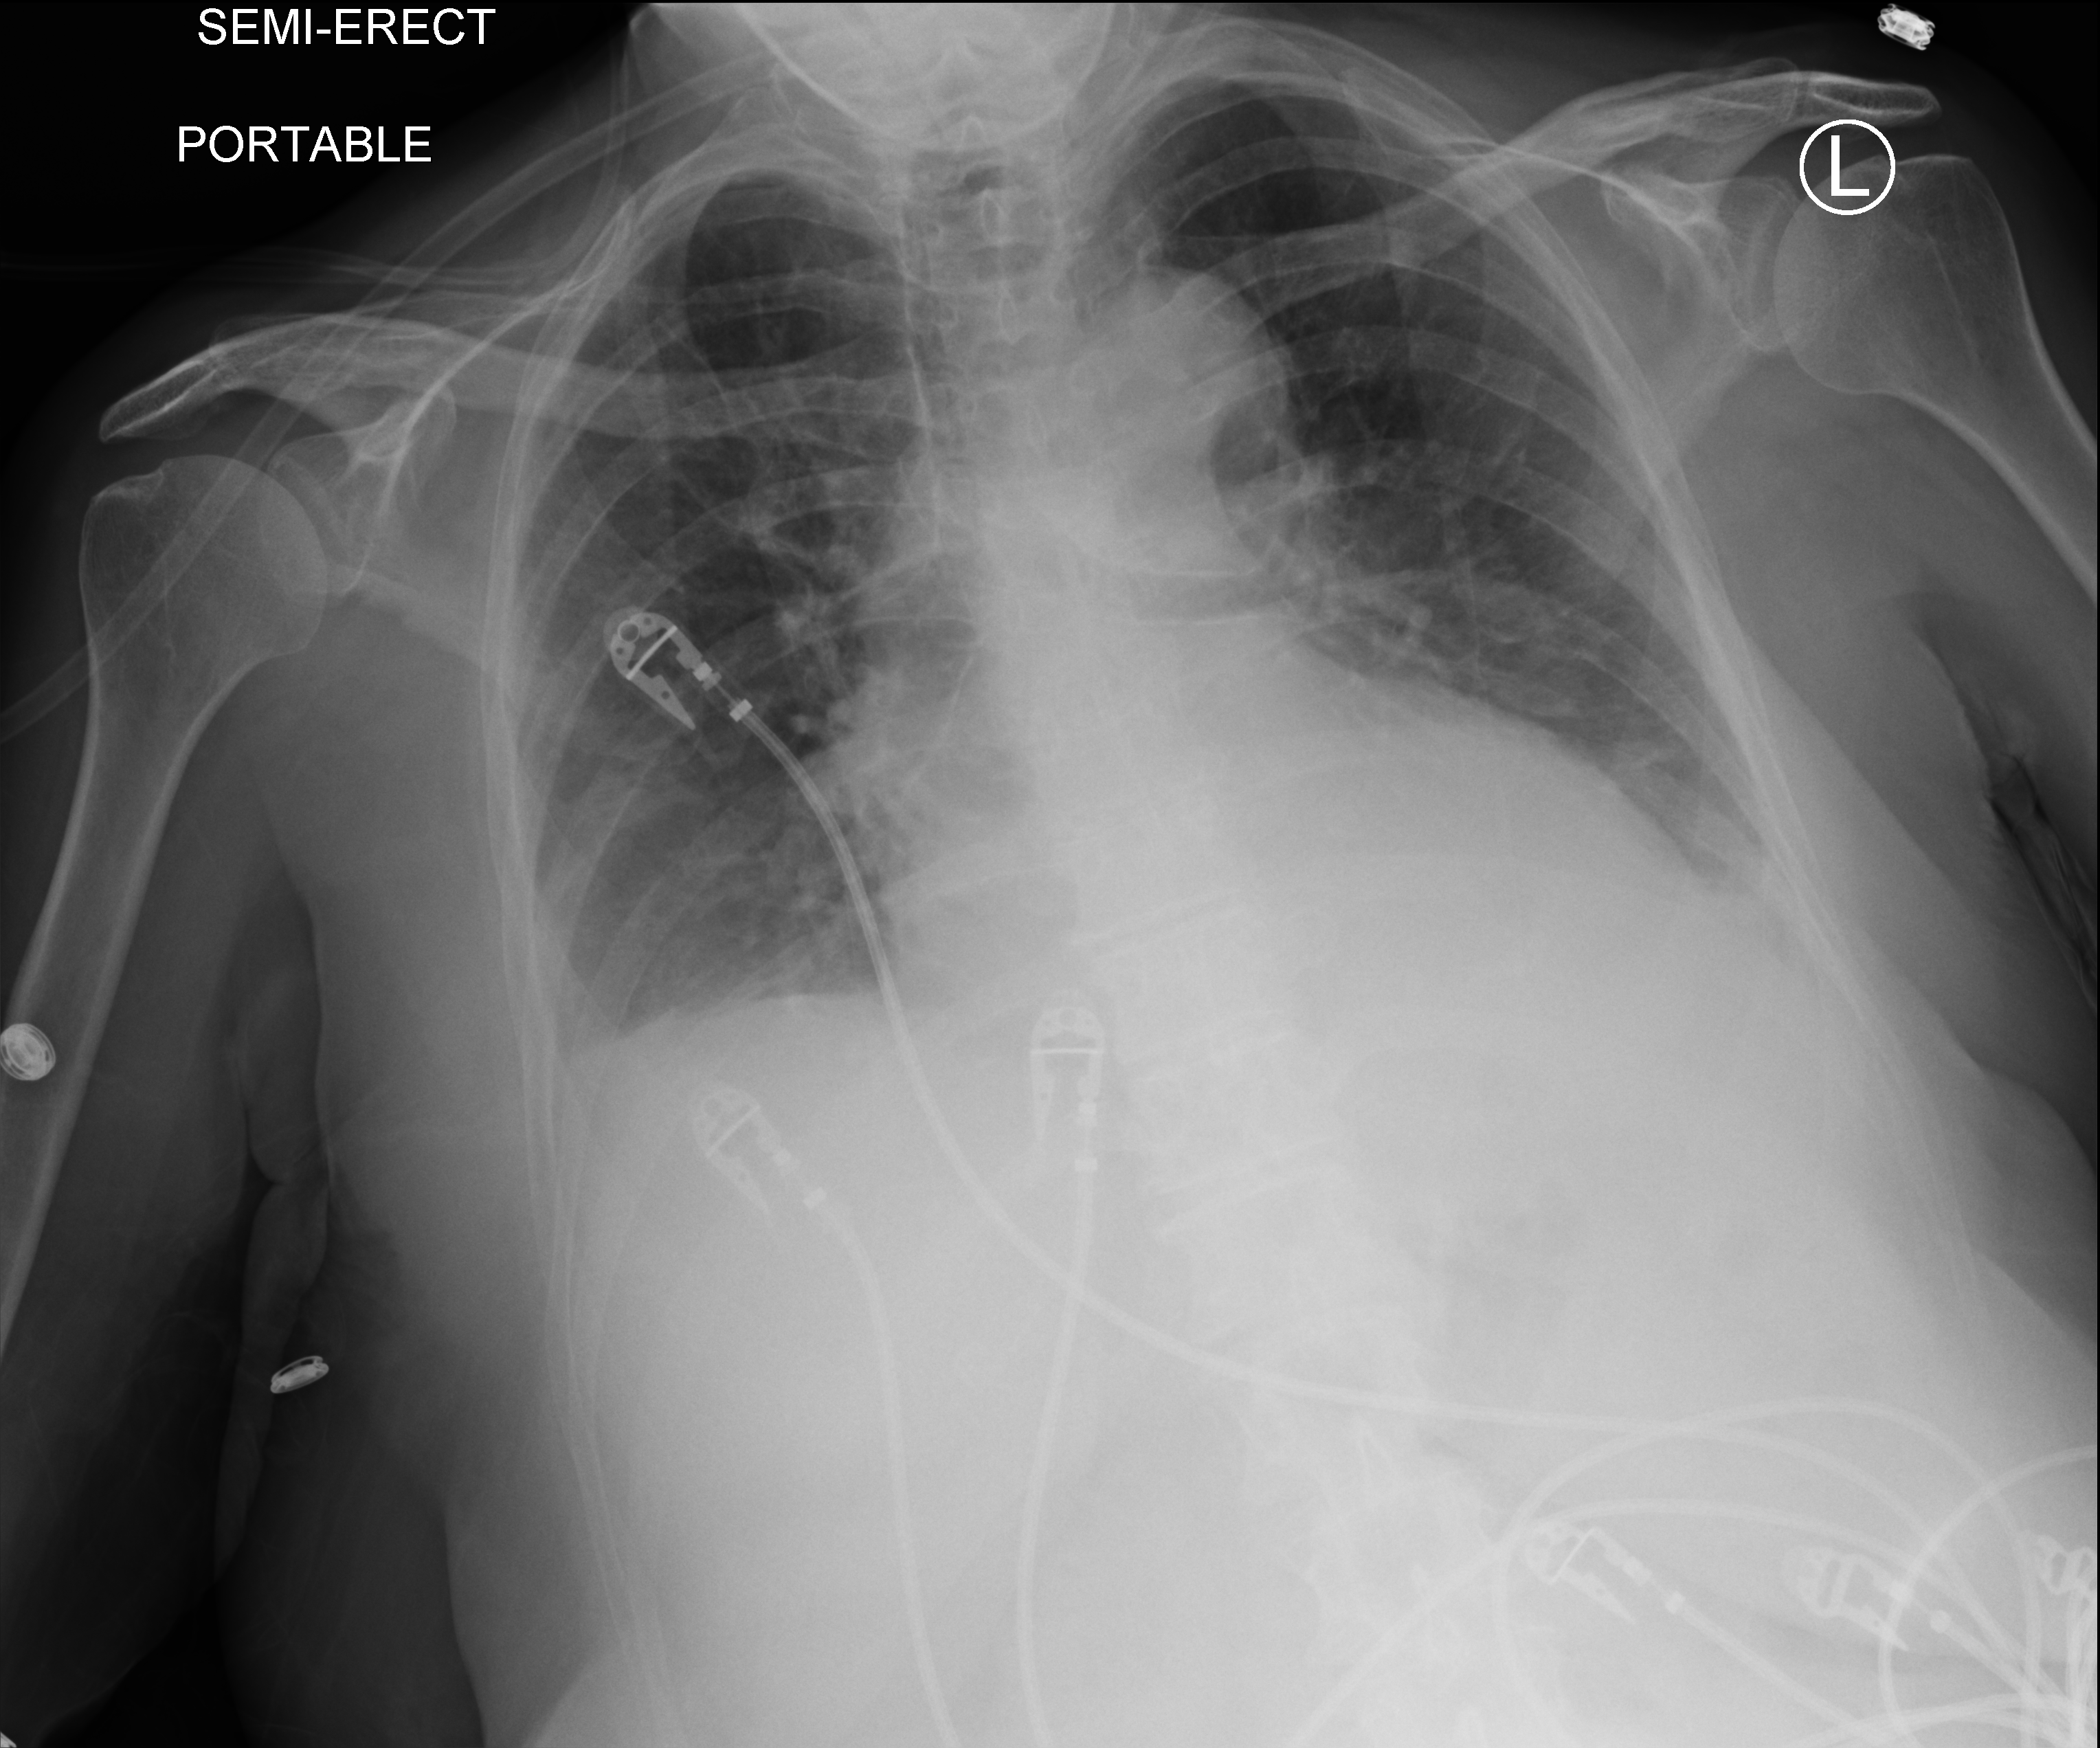
Portable chest radiograph, anteroposterior (AP) projection. Patient hospitalised with COVID-19; female, aged 75–90 years.
Hospital-stay facts (about this admission, not read from this image; timing relative to this image not recorded): mechanically ventilated during this hospital stay: no; length of hospital stay: 21 days; admitted to intensive care during this hospital stay: no.